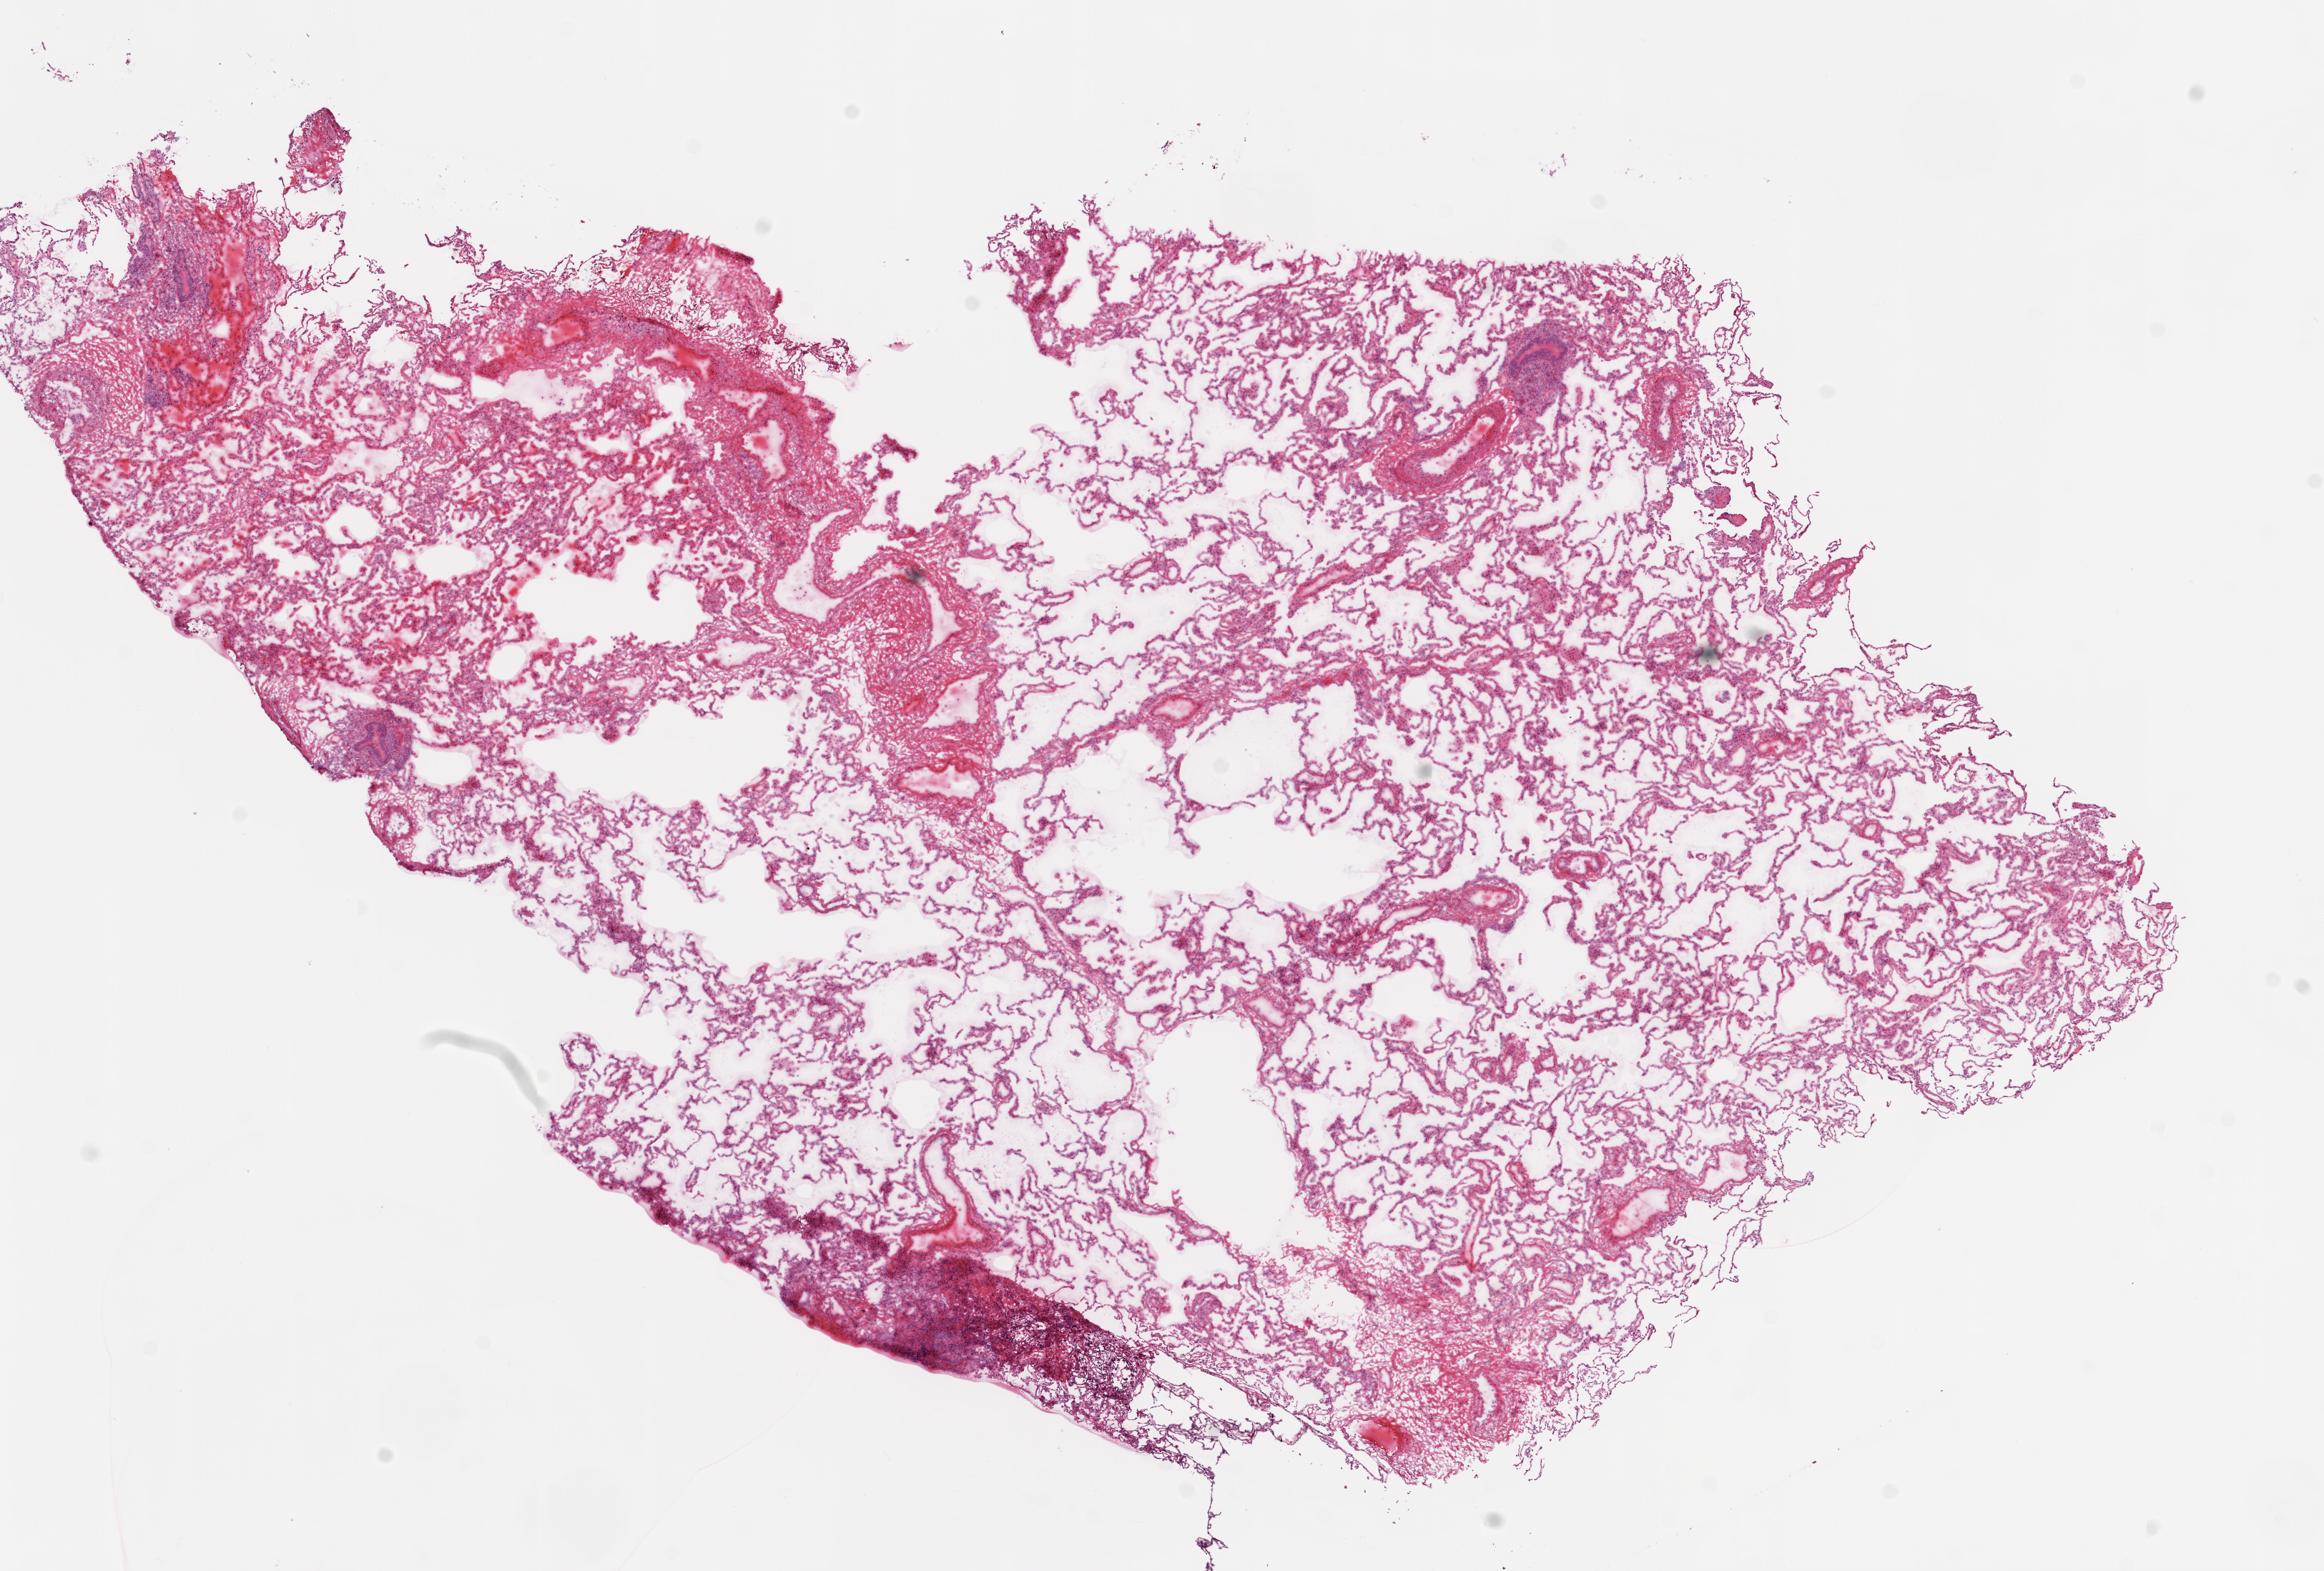
Whole-slide histology image, H&E — a low-resolution overview of the entire scanned area, about 13.0 x 8.8 mm, frozen section from the top of the tissue portion, sample: solid tissue normal (non-tumour tissue), lung. Male, age 64 years at initial diagnosis.
This section: solid tissue normal (non-tumour) sample from the same patient. Patient diagnosis: Squamous cell carcinoma, NOS (upper lobe, lung).